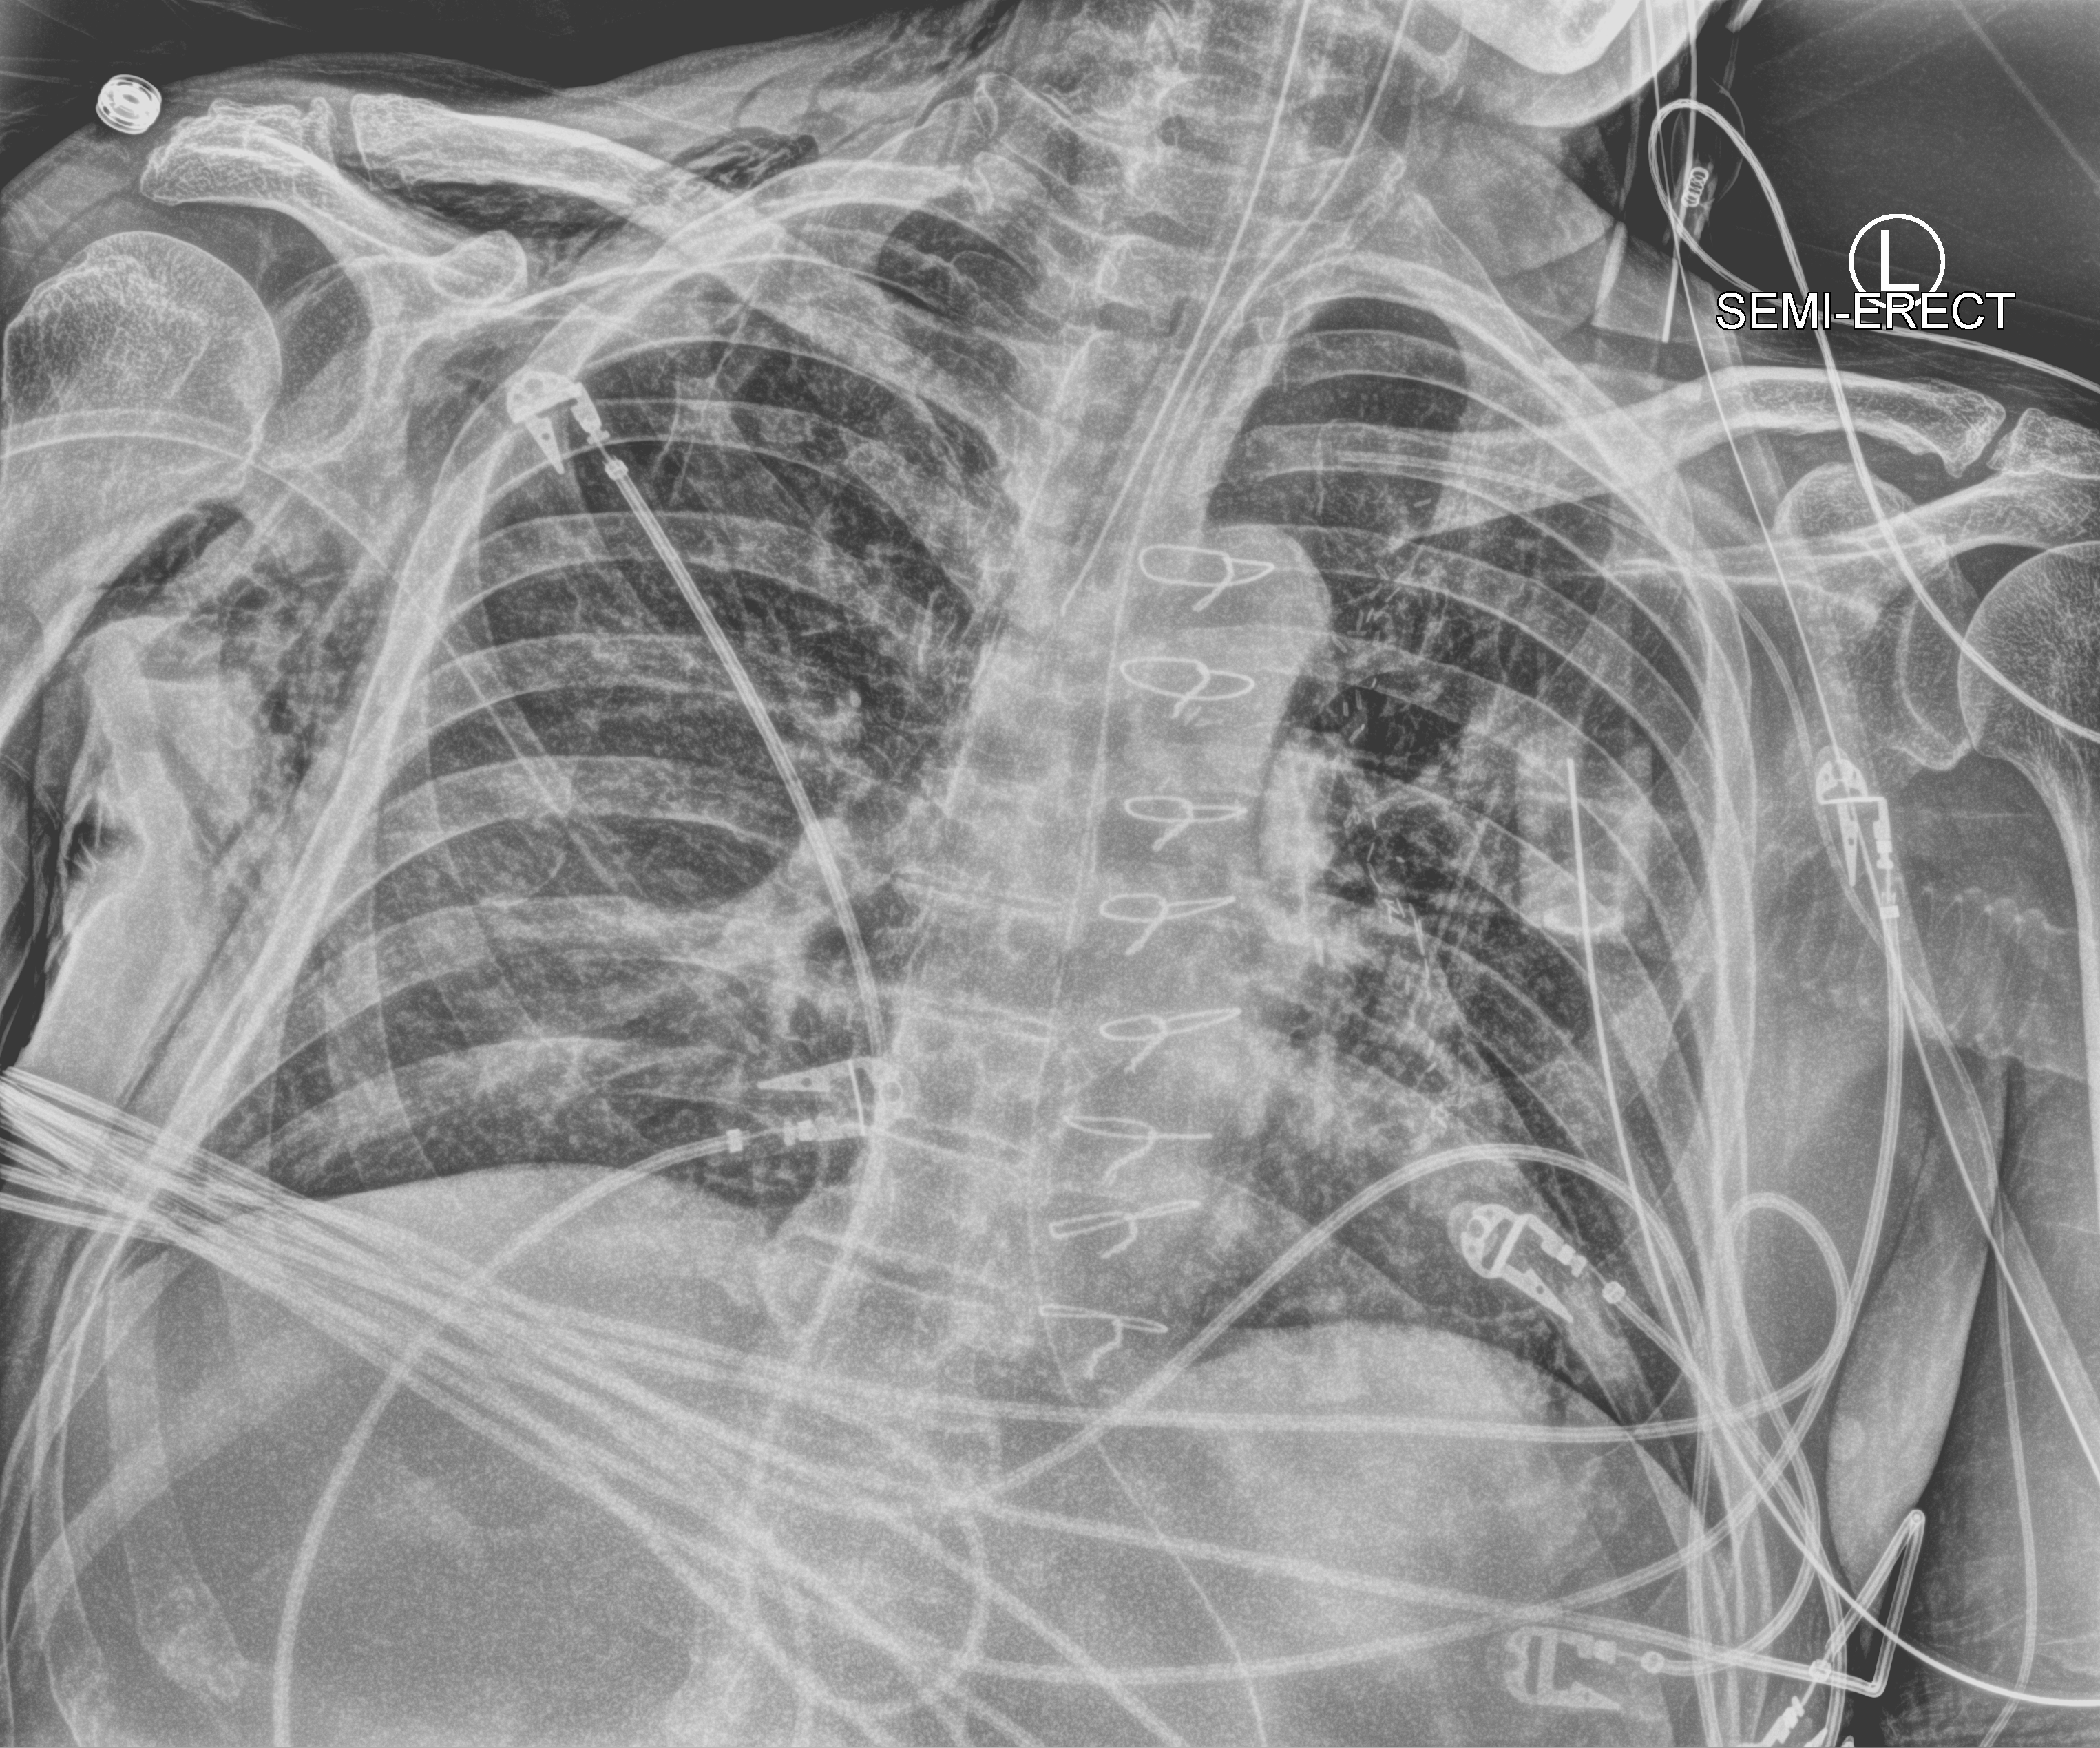
Chest X-ray (portable), anteroposterior (AP) projection. Male patient hospitalised with COVID-19, age 60–74 years.
Admission-level facts for this patient (not findings on this image; timing relative to this image not recorded): mechanically ventilated during this hospital stay: yes.